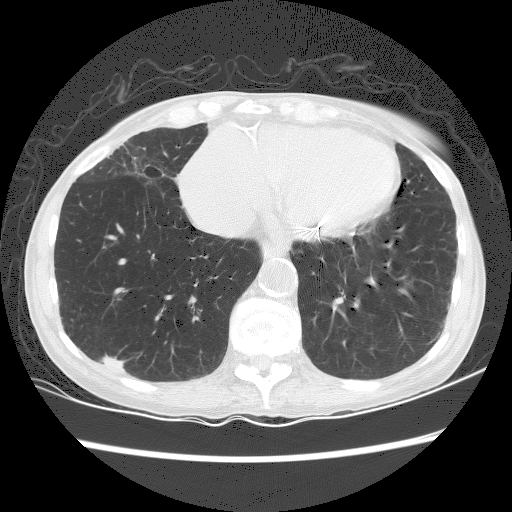
Low-dose screening chest CT, axial slice. Baseline screening round. Lung window (W 1500 / L -600 HU). Female, age 70 years at enrolment. Current smoker at enrolment.
- Lesion marked by an expert reader, box from (x=92, y=345) to (x=144, y=385) px.
- The screening reader recorded 2 non-calcified nodules or masses ≥4 mm on this exam (right lower lobe, left lower lobe); which of them this box marks is not recorded.
- Later outcome: lung cancer diagnosed 125 days after this screen — squamous cell carcinoma, NOS, right lower lobe, well differentiated (G1), stage IA (AJCC 6th edition), 25 mm at pathology.